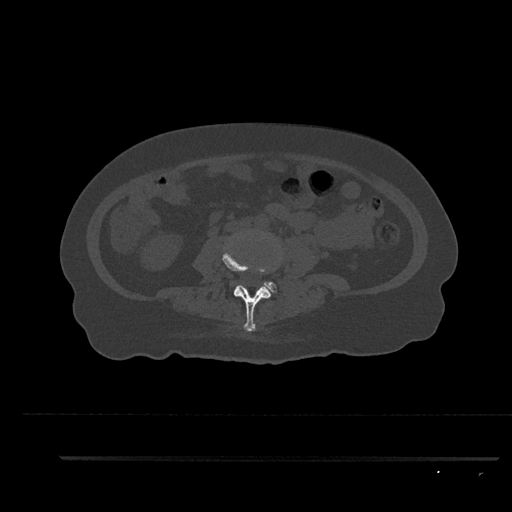
CT including the spine, one axial slice. Position 64 of 797 along the scan axis. Reconstruction kernel Br40s/3. 120 kVp. Bone window (W 1800 / L 400 HU). 0.5 mm slice thickness. 512 × 512 image matrix. Patient: female, 44 years. Case-level facts recorded for this patient, not image findings: primary cancer: renal; vertebrae with lytic lesions (as recorded): L1.
Structures marked on this image (semi-automatically segmented with operator editing):
- L3 vertebra: bounding box [x1, y1, x2, y2] px = [222, 242, 271, 331]
- L4 vertebra: [263, 281, 277, 293]